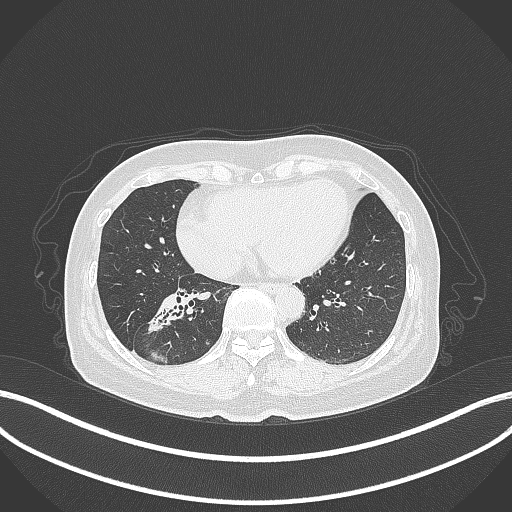
Chest CT, one axial slice. Slice 141 of 429 in the series (ordered by position). 120 kVp. Lung window (W 1500 / L -600 HU). 1 mm slice thickness. 512 × 512 image matrix. Female patient, age 67 years. Case-level facts recorded for this patient, not image findings: clinical TNM (as recorded): T1c N1 M0.
Structures marked on this image (rectangle marked by the reading radiologist):
- lung tumour (recorded histology: adenocarcinoma): bounding box [x1, y1, x2, y2] px = [144, 292, 195, 333]